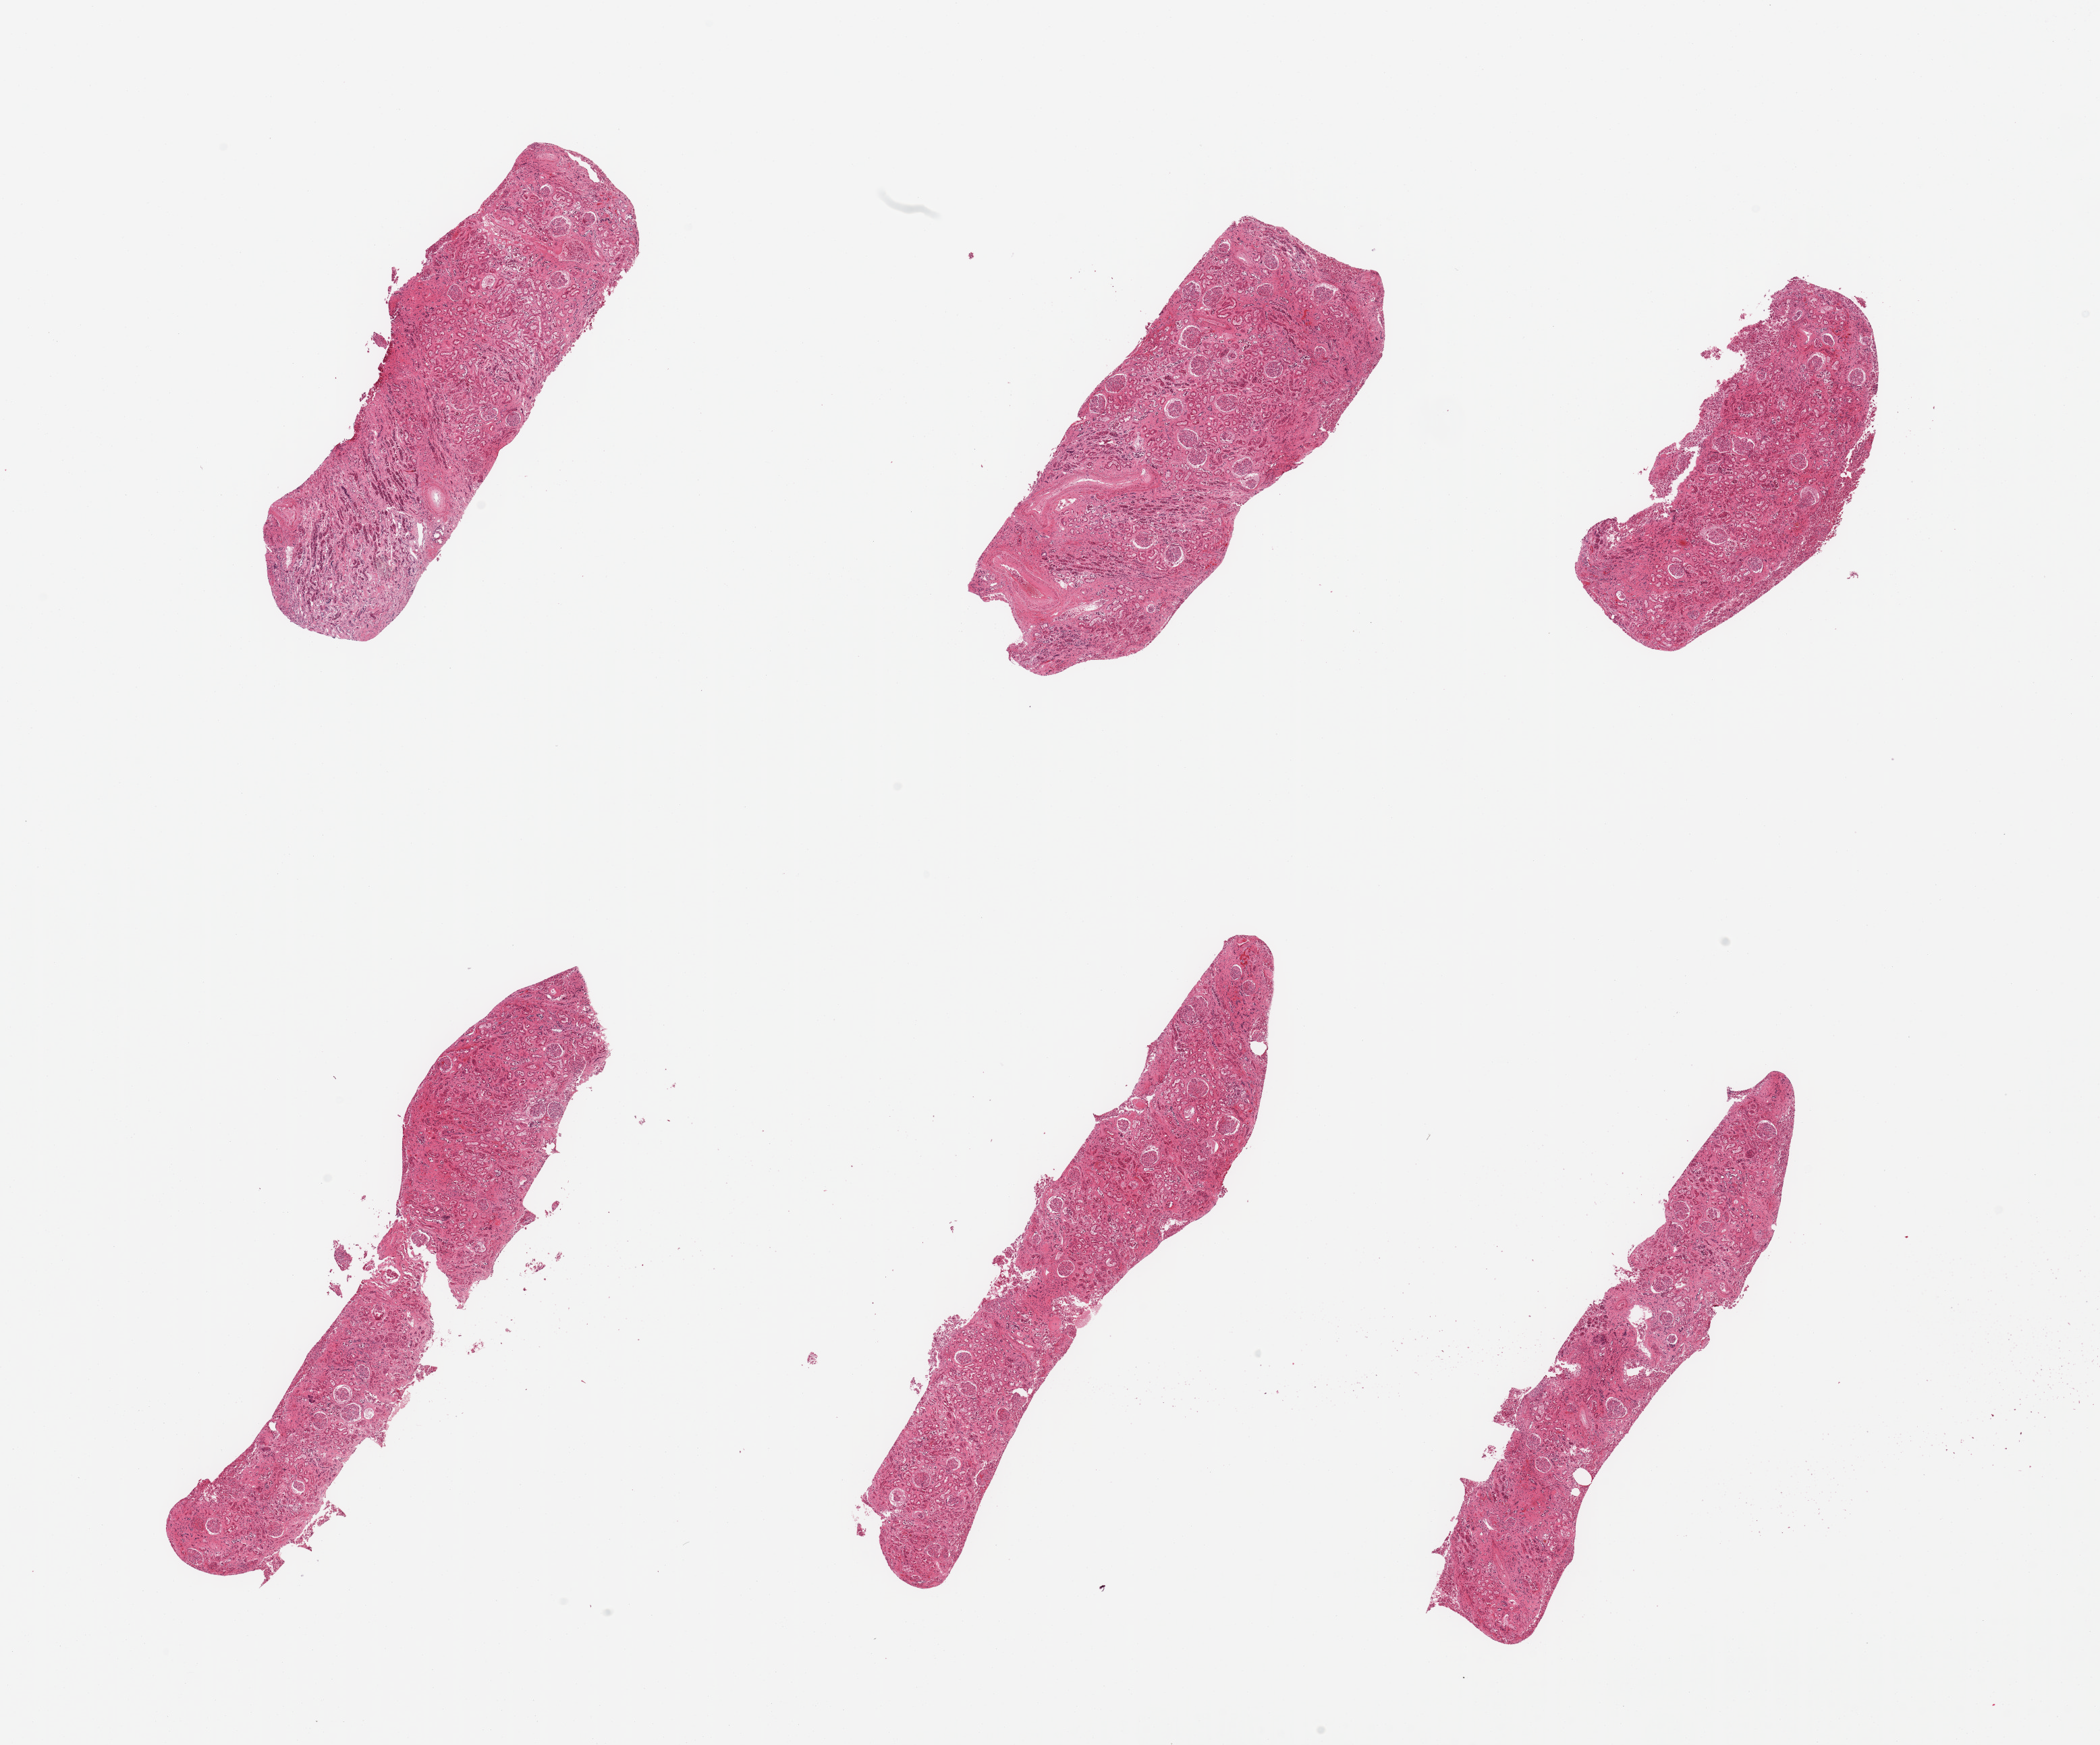
H&E whole-slide image, whole scanned area (about 24.6 x 20.5 mm, acquisition: 20x scan) shown as a low-resolution overview, PAXgene-fixed, paraffin-embedded tissue, sampled site (target tissue): renal cortex, tissue donor sample. Donor: male.
Pathologist's review note for this sample: 6 pieces; scattered arteriolar sclerosis & interstitial fibrosis.